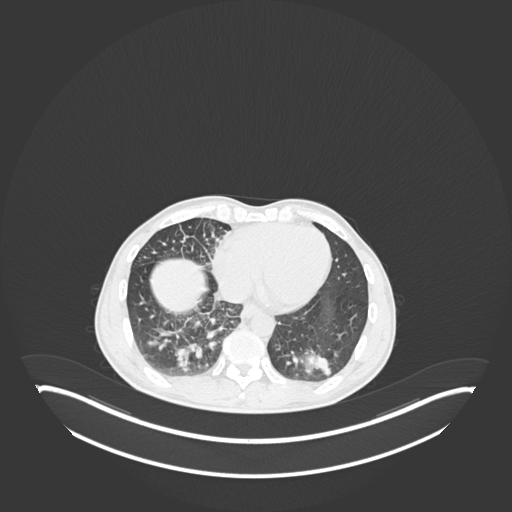
Chest CT, one axial slice; slice 67 of 237 in the series (ordered by position); 120 kVp; lung window (W 1500 / L -600 HU); 1 mm slice thickness; 512 × 512 image matrix, field of view 500 × 500 mm. Male patient, age 49 years. From the clinical record (not read from this slice): clinical TNM (as recorded): T2b N1 M0.
Annotated regions visible in this slice (bounding box drawn by a radiologist):
- lung tumour (recorded histology: adenocarcinoma): bounding box (x1, y1, x2, y2) in pixels: (295, 343, 333, 378)